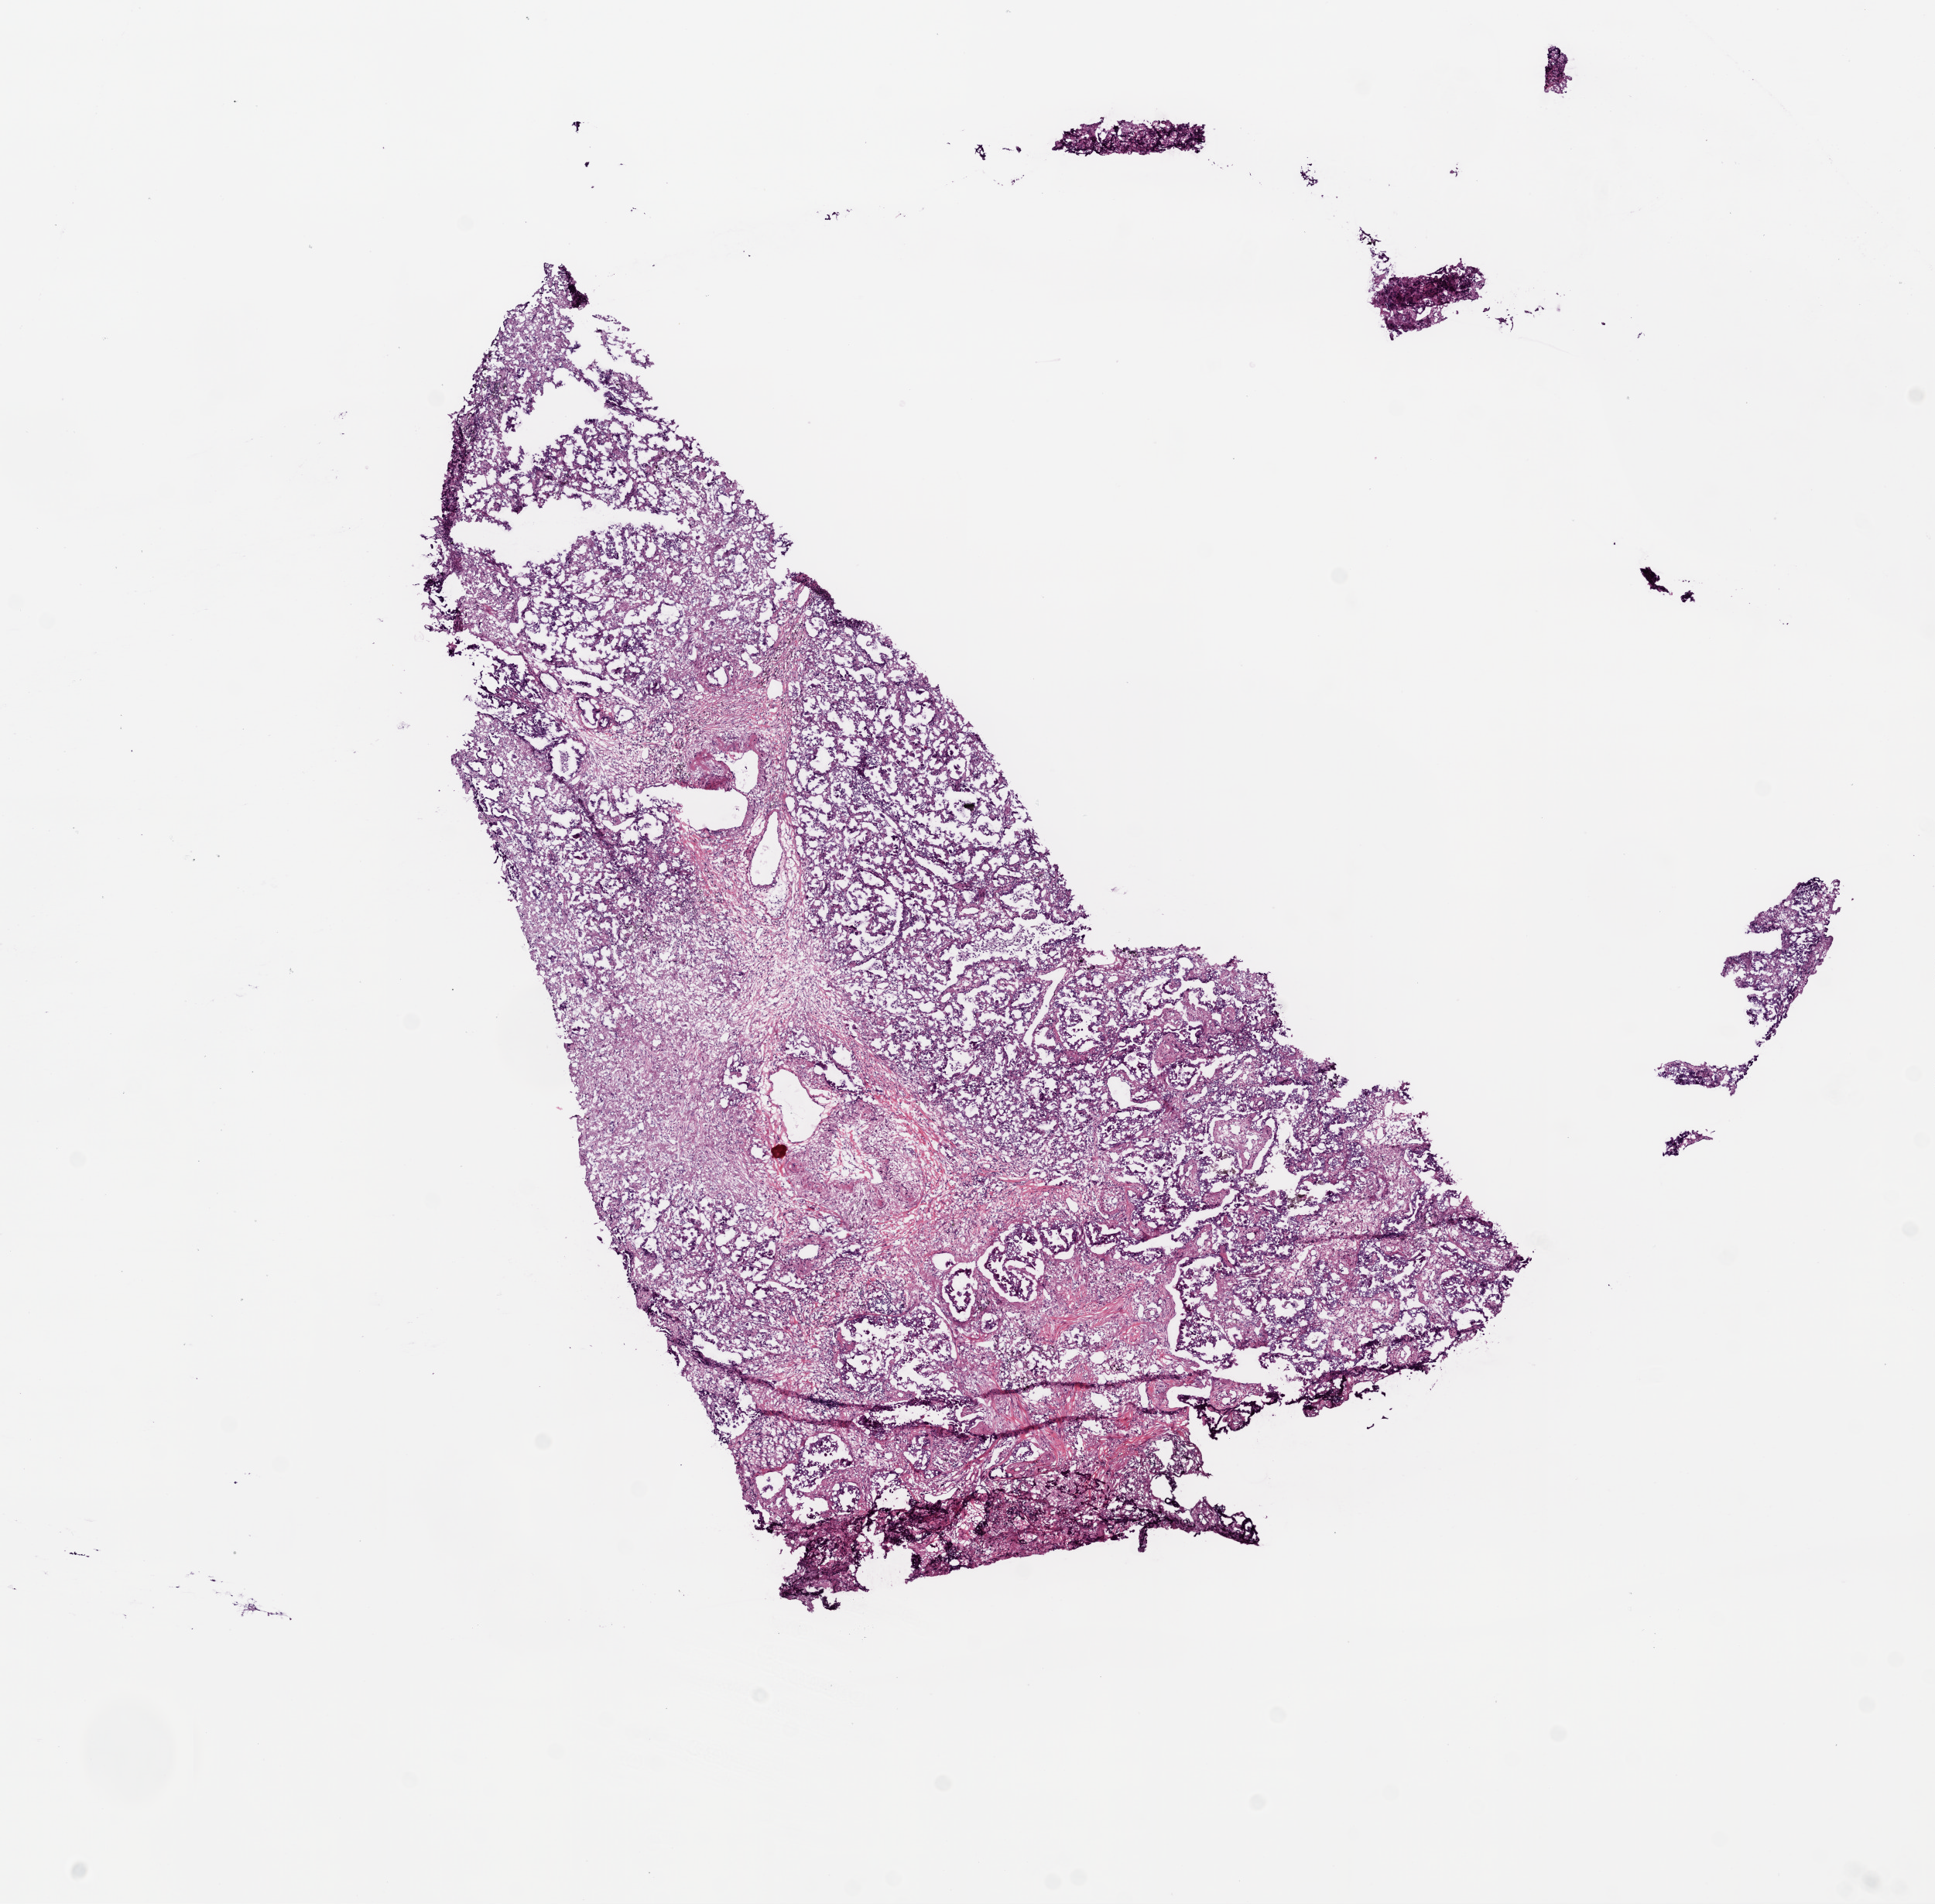
Hematoxylin and eosin (H&E) stained whole-slide image — a low-resolution overview of the entire scanned area, about 10.0 x 9.9 mm; frozen section from the bottom of the tissue portion; sample: primary tumour, lung. Female patient; age at initial diagnosis 45 years. Composition of this section per pathologist review: tumour cells 80%, tumour nuclei 70%, normal cells 0%, stromal cells 20%, necrosis 0%.
* diagnosis: Adenocarcinoma, NOS (upper lobe, lung)
* laterality: left
* AJCC pathologic stage: IIIA